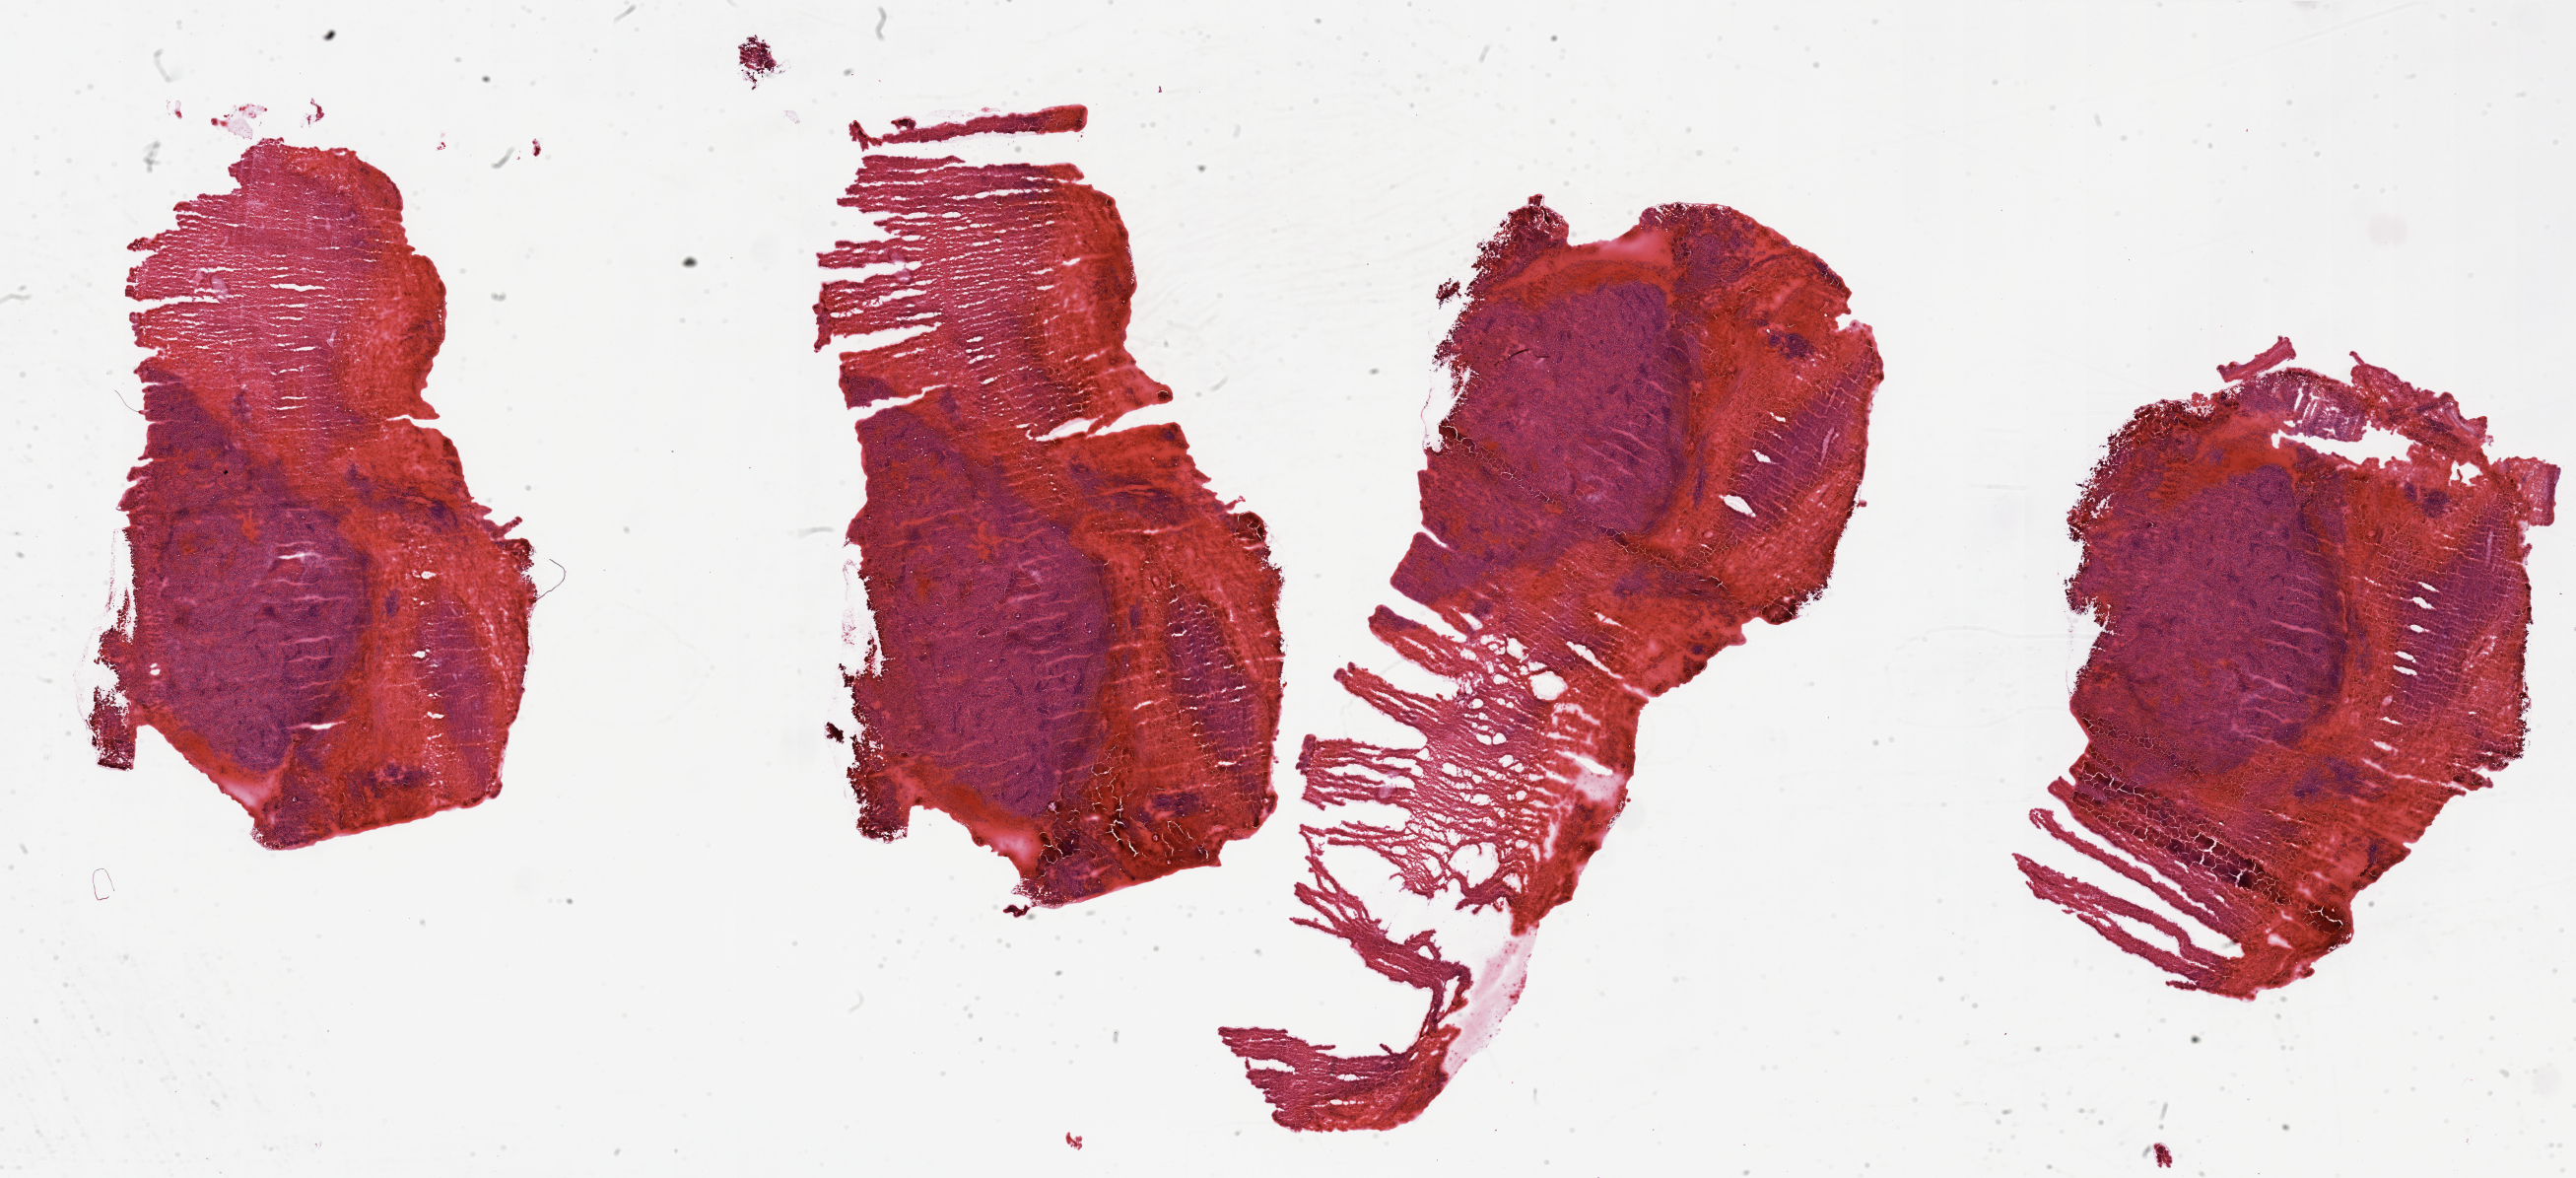
Digitized Hematoxylin and eosin (H&E) stained tissue section (whole slide) — a low-resolution overview of the entire scanned area, about 41.3 x 18.9 mm (from a 20x scan). Kidney, tumour tissue. 68-year-old male patient. Histologic grade: G3 (poorly differentiated).
Diagnosis: Renal cell carcinoma, NOS. Primary tumour site (as recorded): lower pole. AJCC pathologic stage: I.